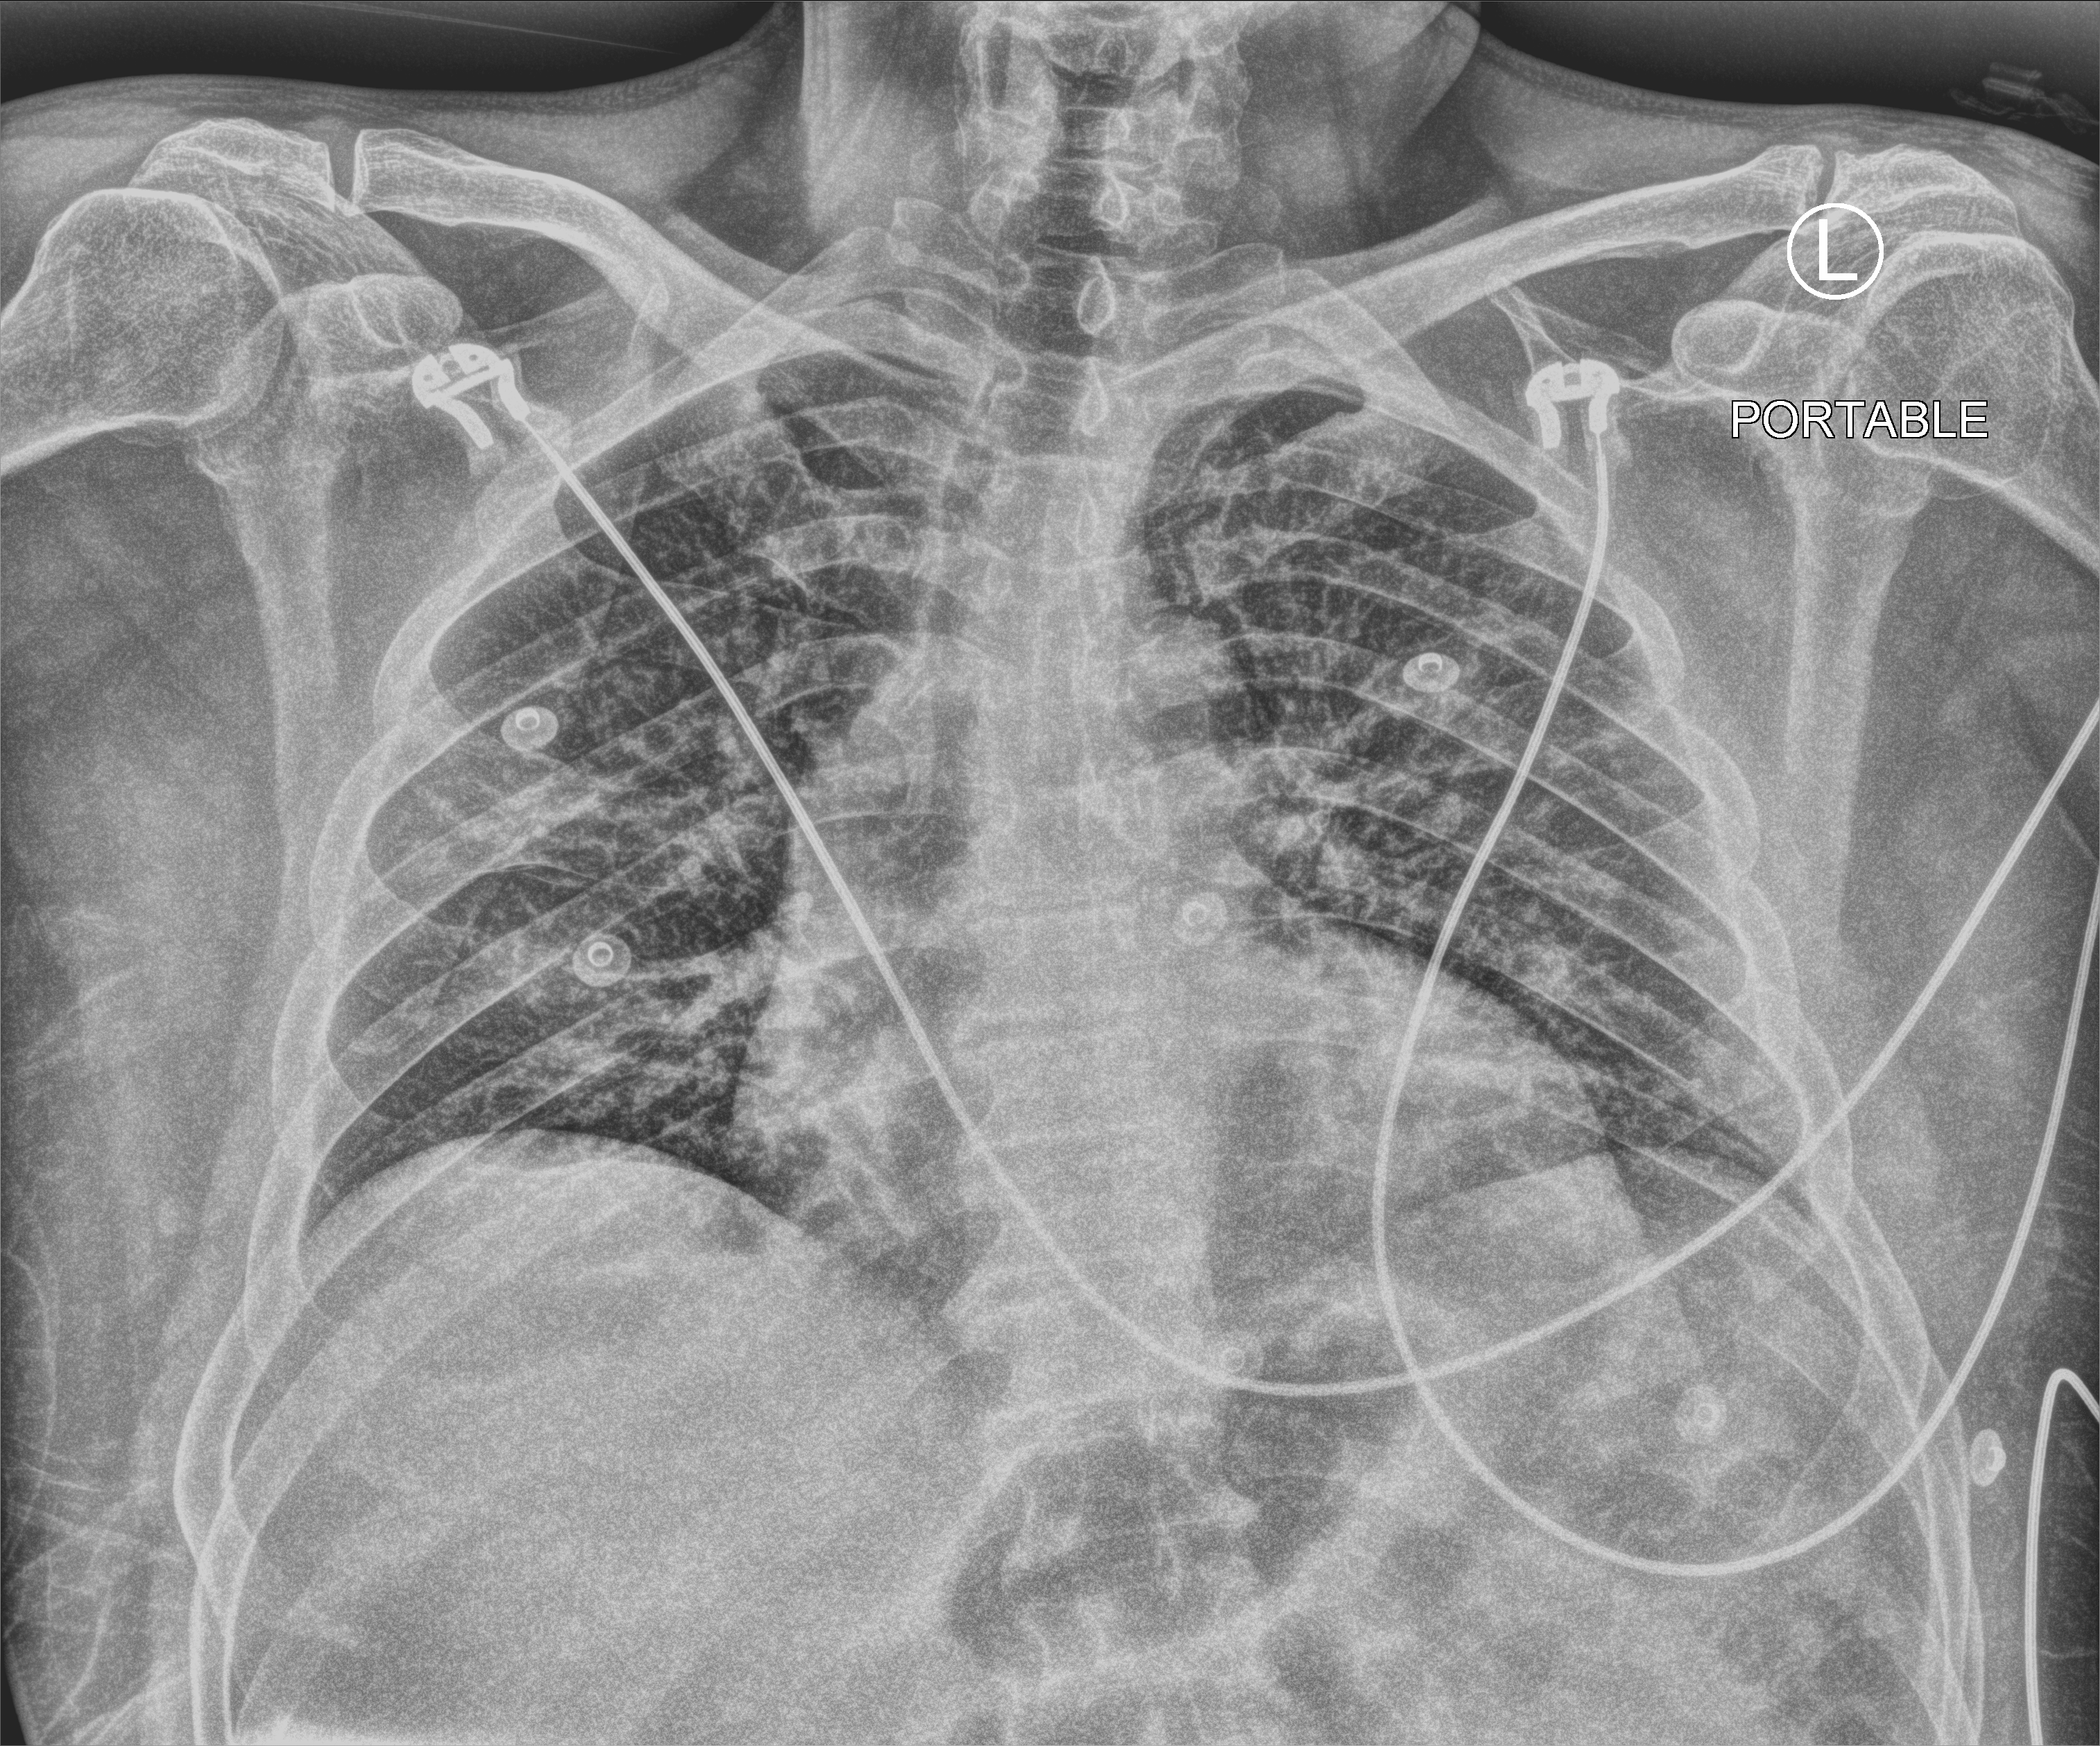
Bedside chest radiograph (computed radiography). Patient hospitalised with COVID-19; male, aged 18–59 years.
Admission-level facts for this patient (not findings on this image; timing relative to this image not recorded):
- admitted to intensive care during this hospital stay: no
- other chronic lung disease (admission record): no
- length of hospital stay: 9 days